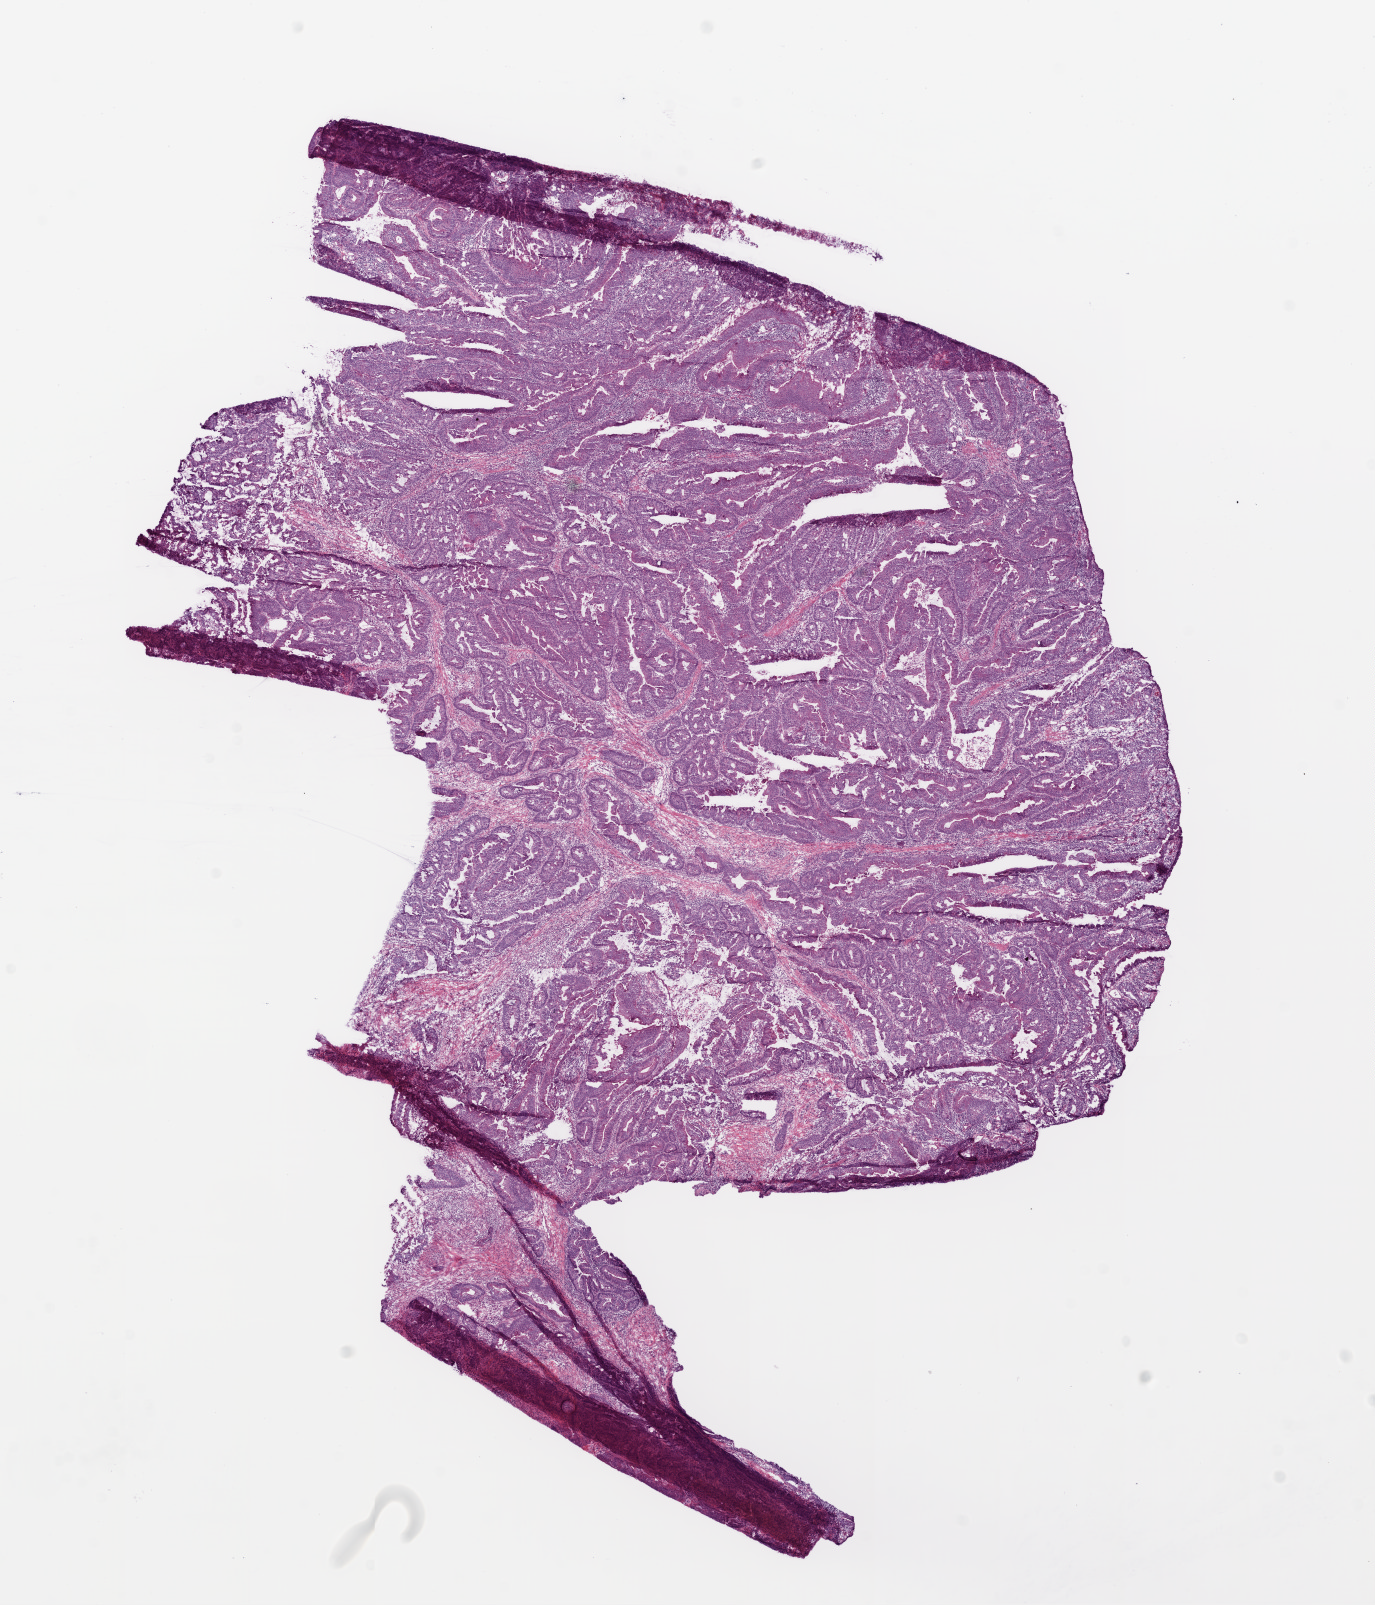
Whole-slide histology image, H&E-stained, shown as a low-resolution overview of the whole scanned area (about 11.0 x 12.9 mm, slide scanned at 20x); frozen section from the bottom of the tissue portion; colon, primary tumour sample. Patient: male, age at initial diagnosis 84 years. Pathologist review of this section (percent, as recorded): tumour cells 94%, tumour nuclei 96%, normal cells 0%, stromal cells 5%, necrosis 1%.
Lymph nodes positive (case pathology): 5 of 19 examined. AJCC pathologic stage: IV (6th edition). Diagnosis: Adenocarcinoma, NOS.